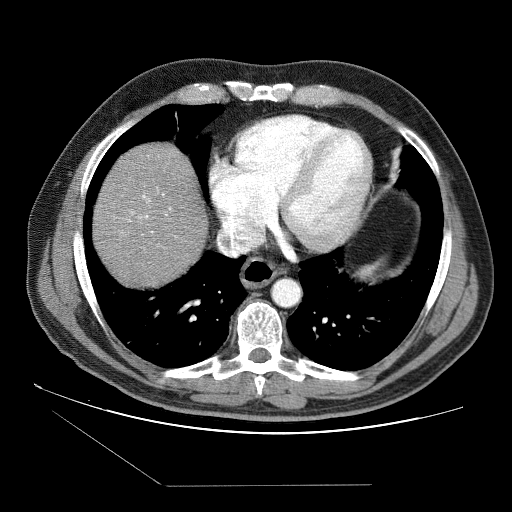
Contrast-enhanced abdominal CT (liver protocol), one axial slice; position 77 of 87 along the scan axis; reconstruction kernel STANDARD; soft-tissue window (W 400 / L 40 HU); 2.5 mm slice thickness; 512 × 512 image matrix. From the clinical record (not read from this slice): diagnosis: hepatocellular carcinoma (patient treated with transarterial chemoembolisation; whether this scan precedes or follows treatment is not stated here); TNM stage (as recorded): Stage-II; Child-Pugh class: B; tumour size: 2.6 cm.
Annotated regions visible in this slice (semi-automatically segmented with operator editing):
- liver parenchyma outside the tumour (the mass and vessels are separate outlines, so this box may not span the whole liver): bounding box (x1, y1, x2, y2) in pixels: (94, 142, 206, 286)
- liver vessels: (128, 195, 170, 233)